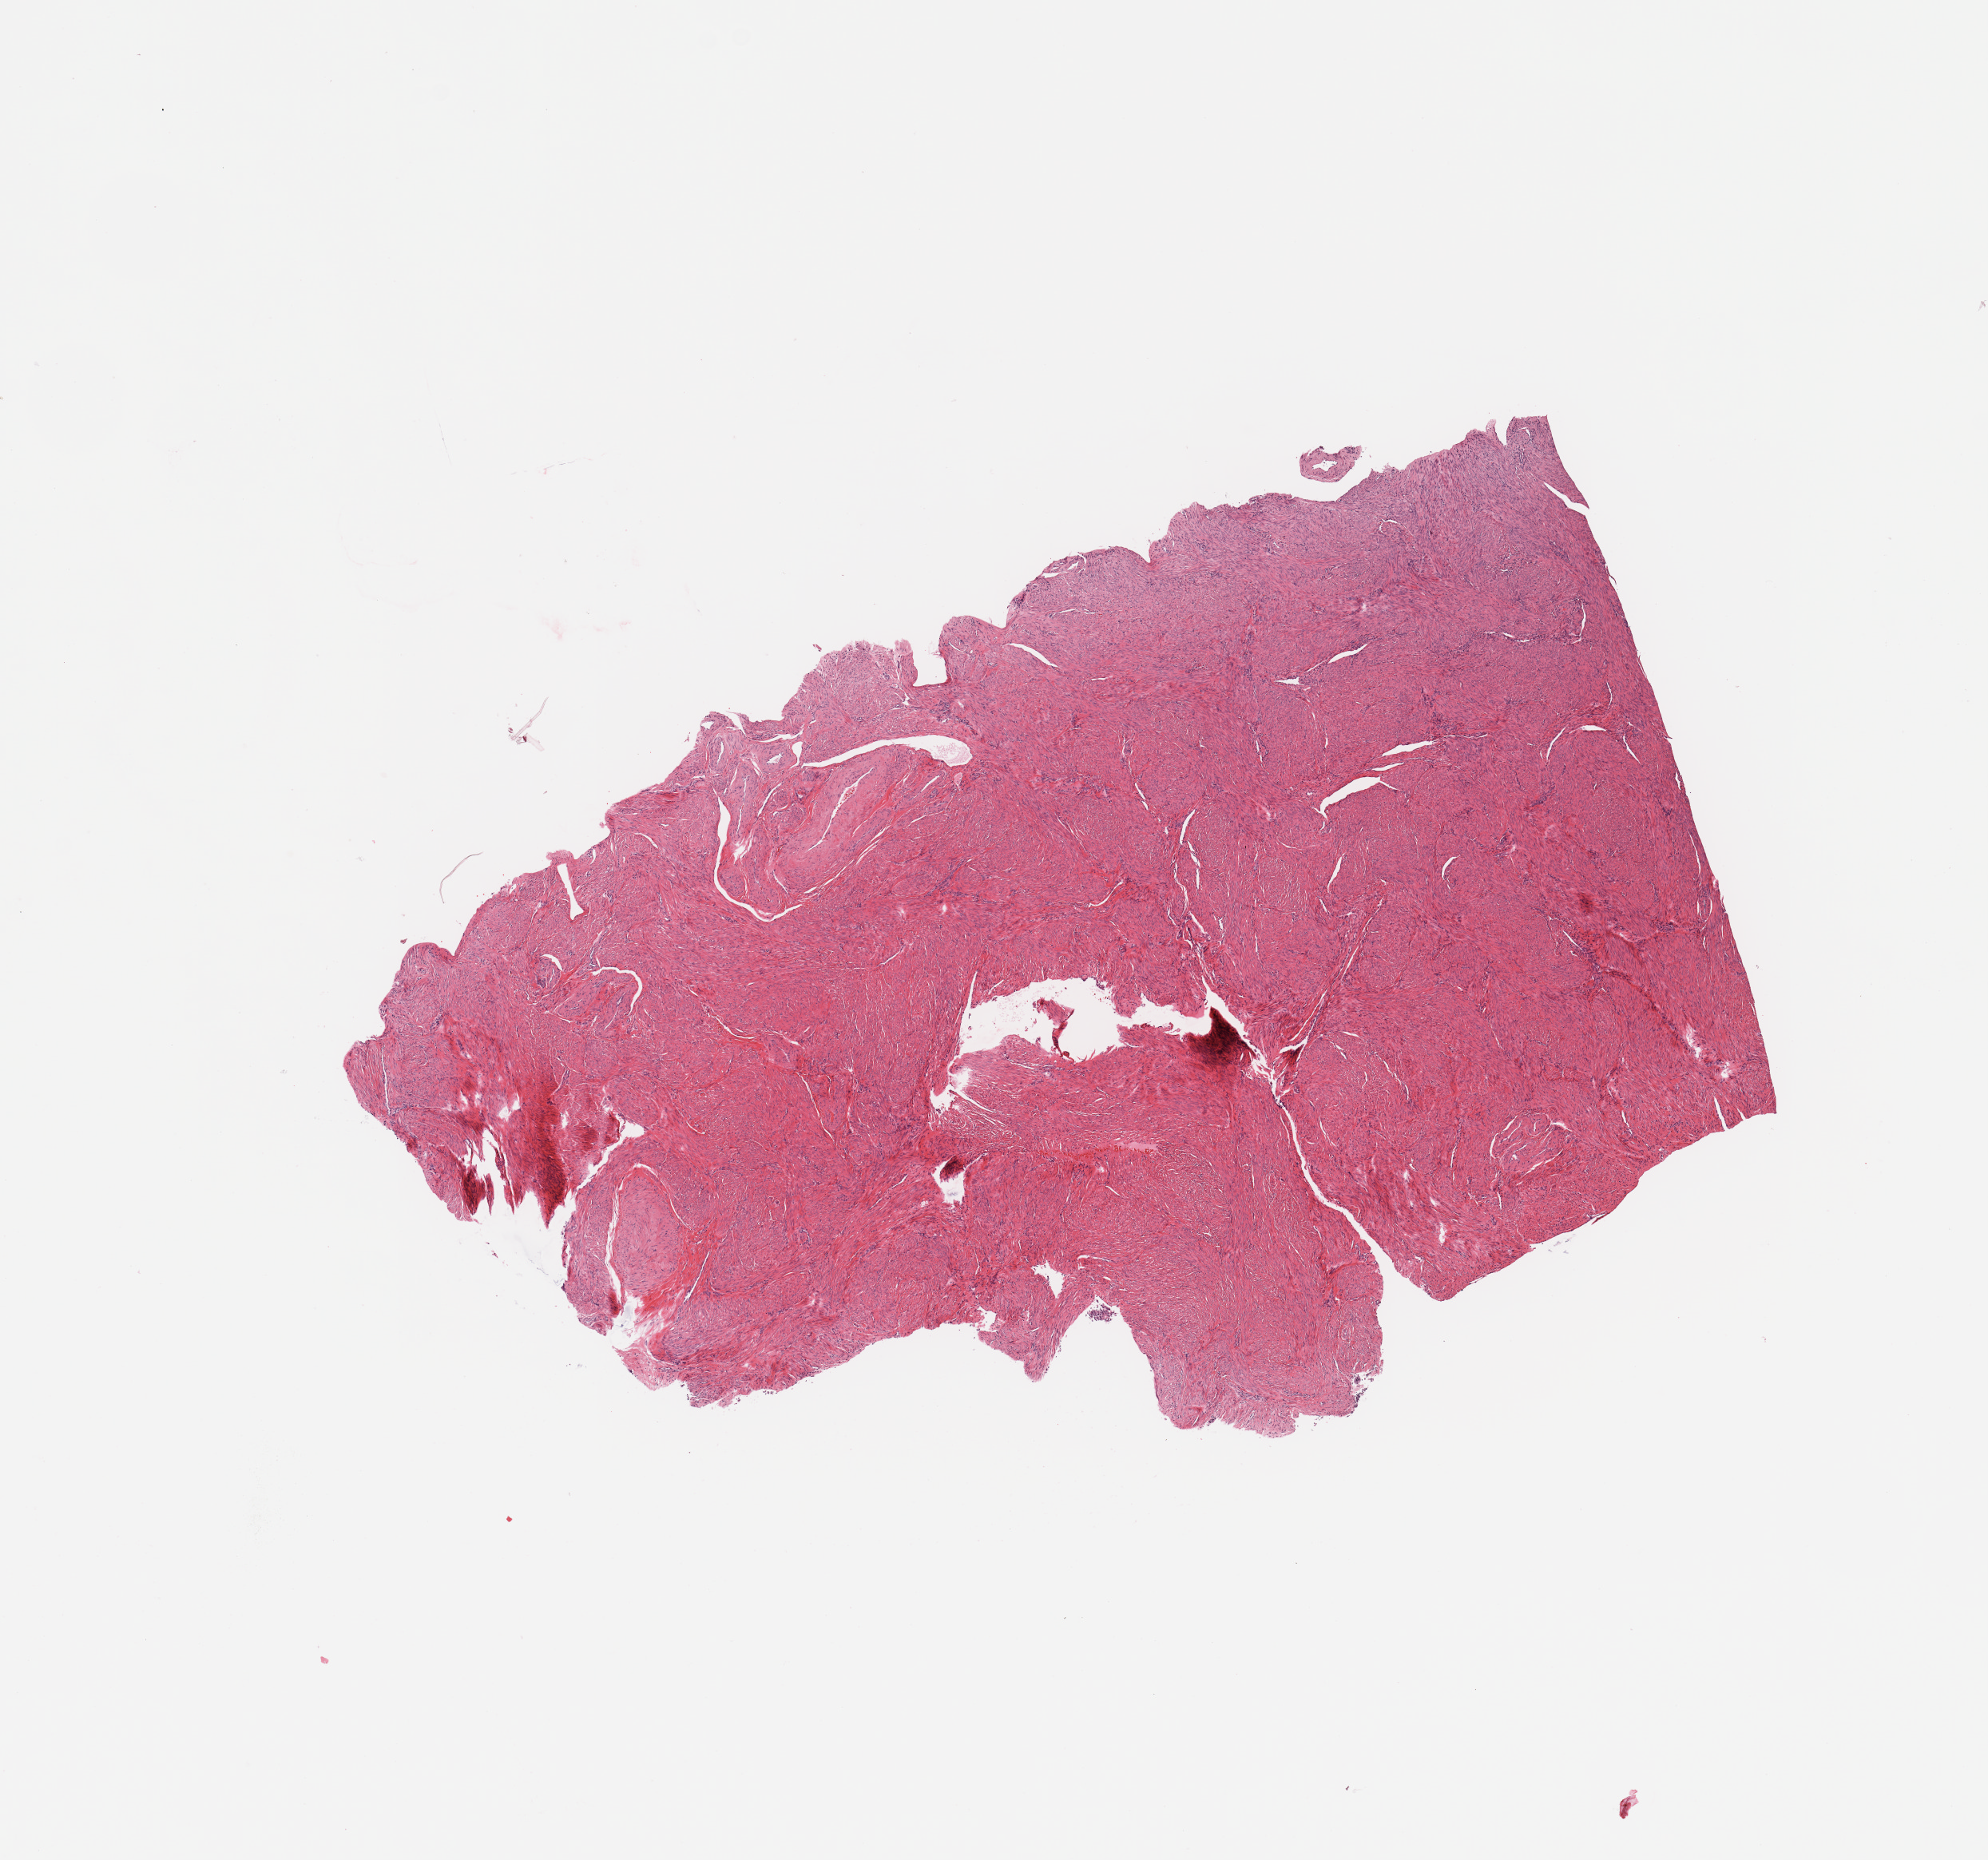
Digitized H&E-stained tissue section (whole slide) — whole scanned area (about 9.8 x 9.2 mm, acquisition: 20x scan) shown as a low-resolution overview. Normal (non-tumour) tissue sample, uterus. 56-year-old female patient.
This section: normal (non-tumour) tissue from the same patient. Patient diagnosis: Endometrioid adenocarcinoma, NOS.